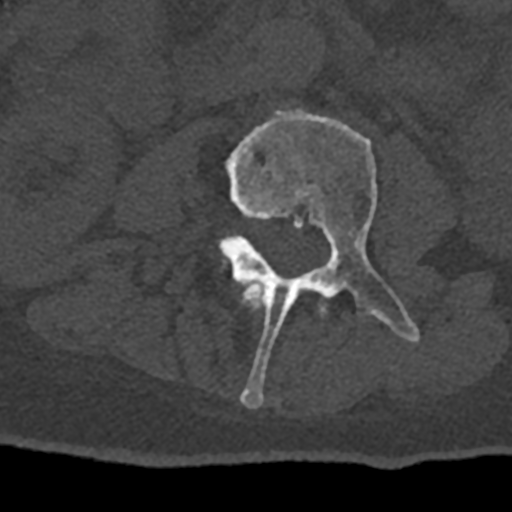
CT including the spine, one axial slice; slice 317 of 797 in the series (ordered by position); bone window (W 1800 / L 400 HU); 0.5 mm slice thickness; 512 × 512 image matrix. Patient: male, 74 years. From the clinical record (not read from this slice): primary cancer: renal; vertebrae with lytic lesions (as recorded): T10, L1, L2, L3, L4, L5.
Outlined on this slice (semi-automatically segmented with operator editing):
- L2 vertebra: box from (x=242, y=283) to (x=327, y=317) px
- L3 vertebra: (x=217, y=109)–(x=420, y=408)